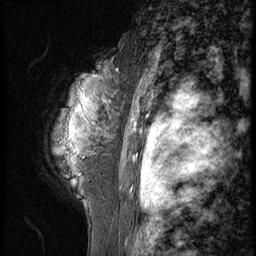
Breast MRI (dynamic contrast-enhanced), one sagittal slice. 3 images stored at this slice position (order not interpretable as contrast timing). 1.5 T. TE 4.2 ms, TR 9 ms. 256 × 256 image matrix, field of view 180 × 180 mm. Patient: female, 50 years. Case-level facts recorded for this patient, not image findings: setting: breast cancer imaged before/during neoadjuvant chemotherapy; receptor status: triple-negative.
Annotated regions visible in this slice (semi-automatically segmented with operator editing):
- analysis volume of interest (the breast-tissue region the enhancement analysis was run in; not a lesion): box from (x=46, y=50) to (x=129, y=191) px
- tumour enhancement mask (voxels above the 140 % enhancement threshold inside the analysis volume of interest): (x=103, y=101)–(x=105, y=103)